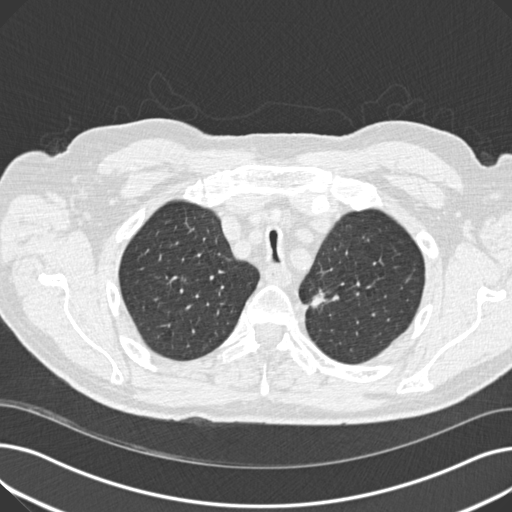
Low-dose screening chest CT, axial slice, third annual screen, lung window (W 1500 / L -600 HU), 2 mm slice thickness, standard (soft-tissue) reconstruction kernel (B30f), slice 42 of 191 in the series. Male participant, aged 70 years at enrolment. Current smoker at enrolment.
- Lesion marked by an expert reader, bounding box <293,276,338,317> (left, top, right, bottom; pixels).
- The screening reader recorded 2 non-calcified nodules or masses ≥4 mm on this exam (left upper lobe, left lower lobe); which of them this box marks is not recorded.
- Official screen result: positive, other.